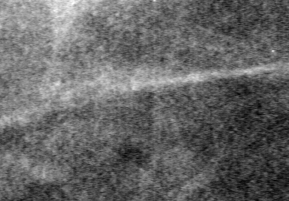
Cropped region of a digitized screen-film mammogram centred on a radiologist-marked abnormality; right breast; CC view; BI-RADS breast density category 3 (scale 1–4).
Finding: calcifications, morphology pleomorphic, distribution clustered; BI-RADS assessment category 4; pathology (as recorded): benign.